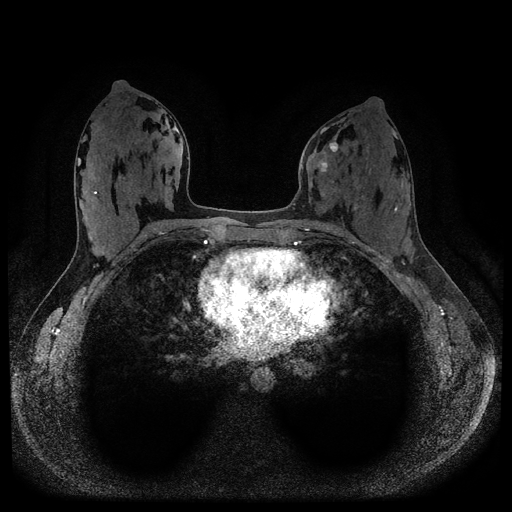
Breast MRI (dynamic contrast-enhanced, multi-phase), one axial slice. Position 49 of 116 along the scan axis. Dynamic contrast-enhanced series, time point 2 of 5 at this slice position (early post-contrast). 1.5 T. TE 2.6 ms, TR 5.3 ms. 2 mm slice thickness. 512 × 512 image matrix, field of view 350 × 350 mm. Patient: female, 33 years.
Annotated regions visible in this slice (semi-automatically segmented with operator editing):
- breast lesion (labelled 'tumour' in the annotation; benign lesions carry a separate 'benign' label): bounding box [x1, y1, x2, y2] px = [318, 138, 342, 173]